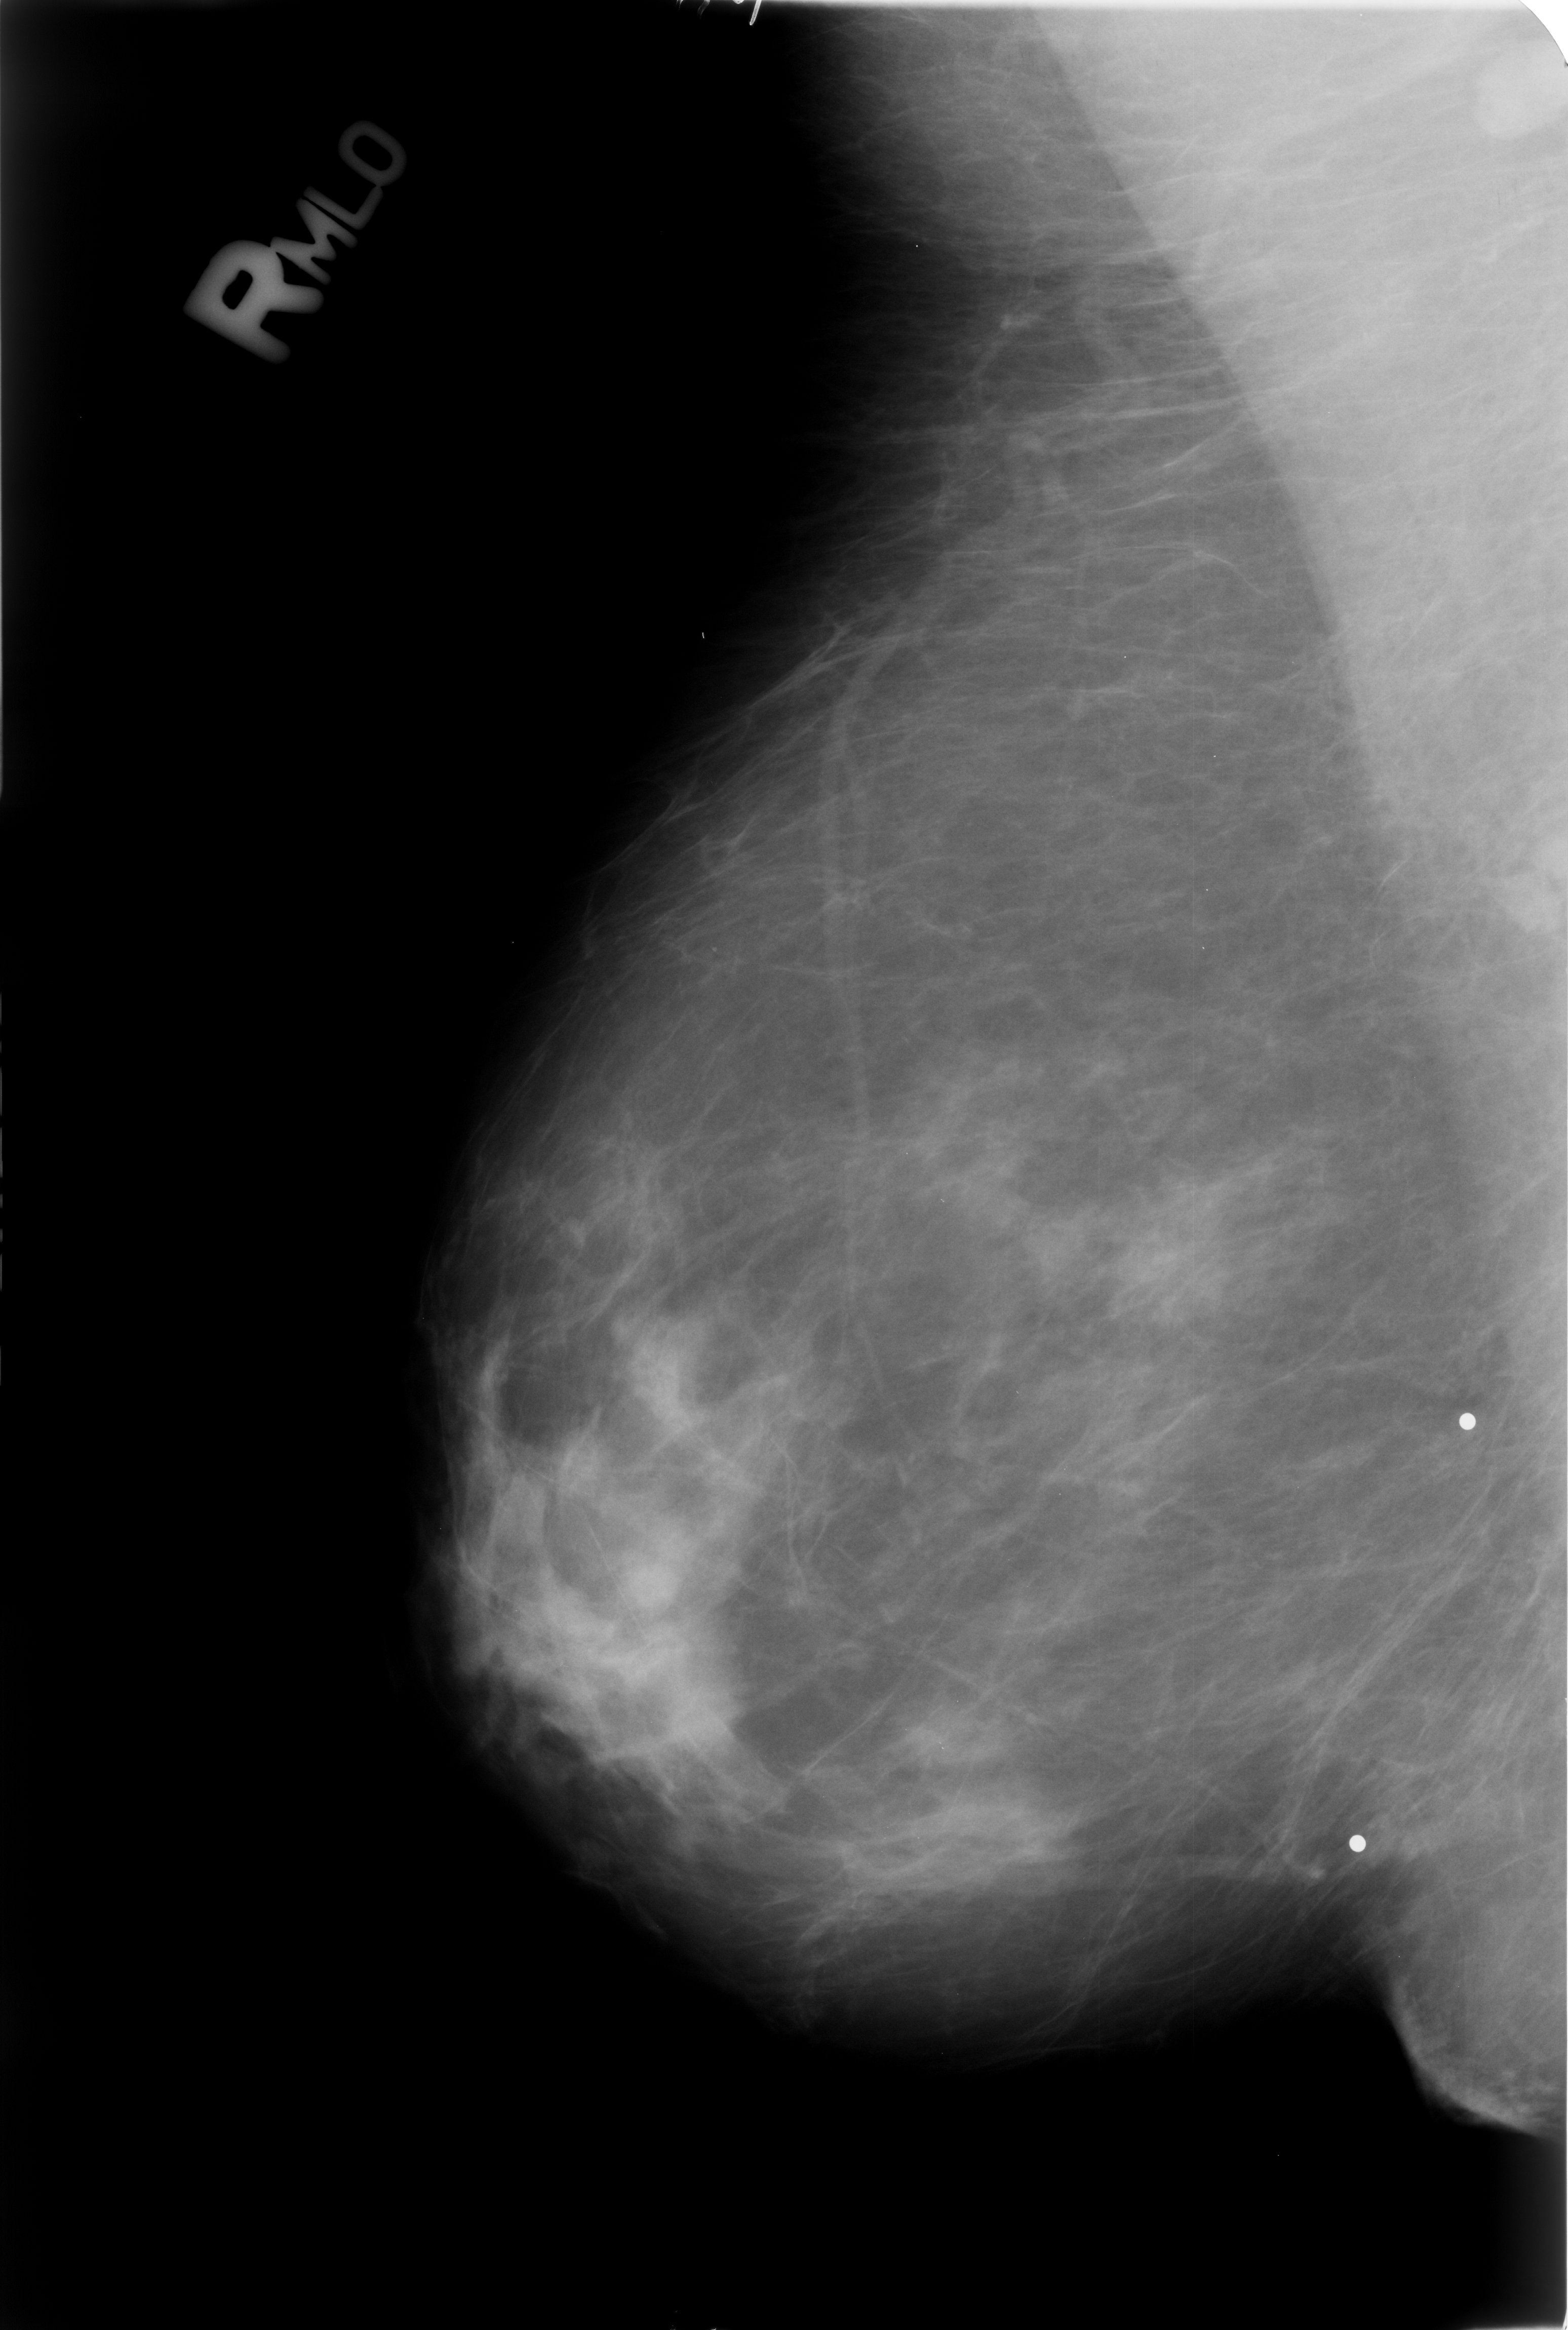
Digitized screen-film mammogram, right breast, mediolateral oblique (MLO) view.
- Finding: calcifications, morphology punctate; BI-RADS assessment category 2; benign; no additional work-up was recommended (benign without callback).